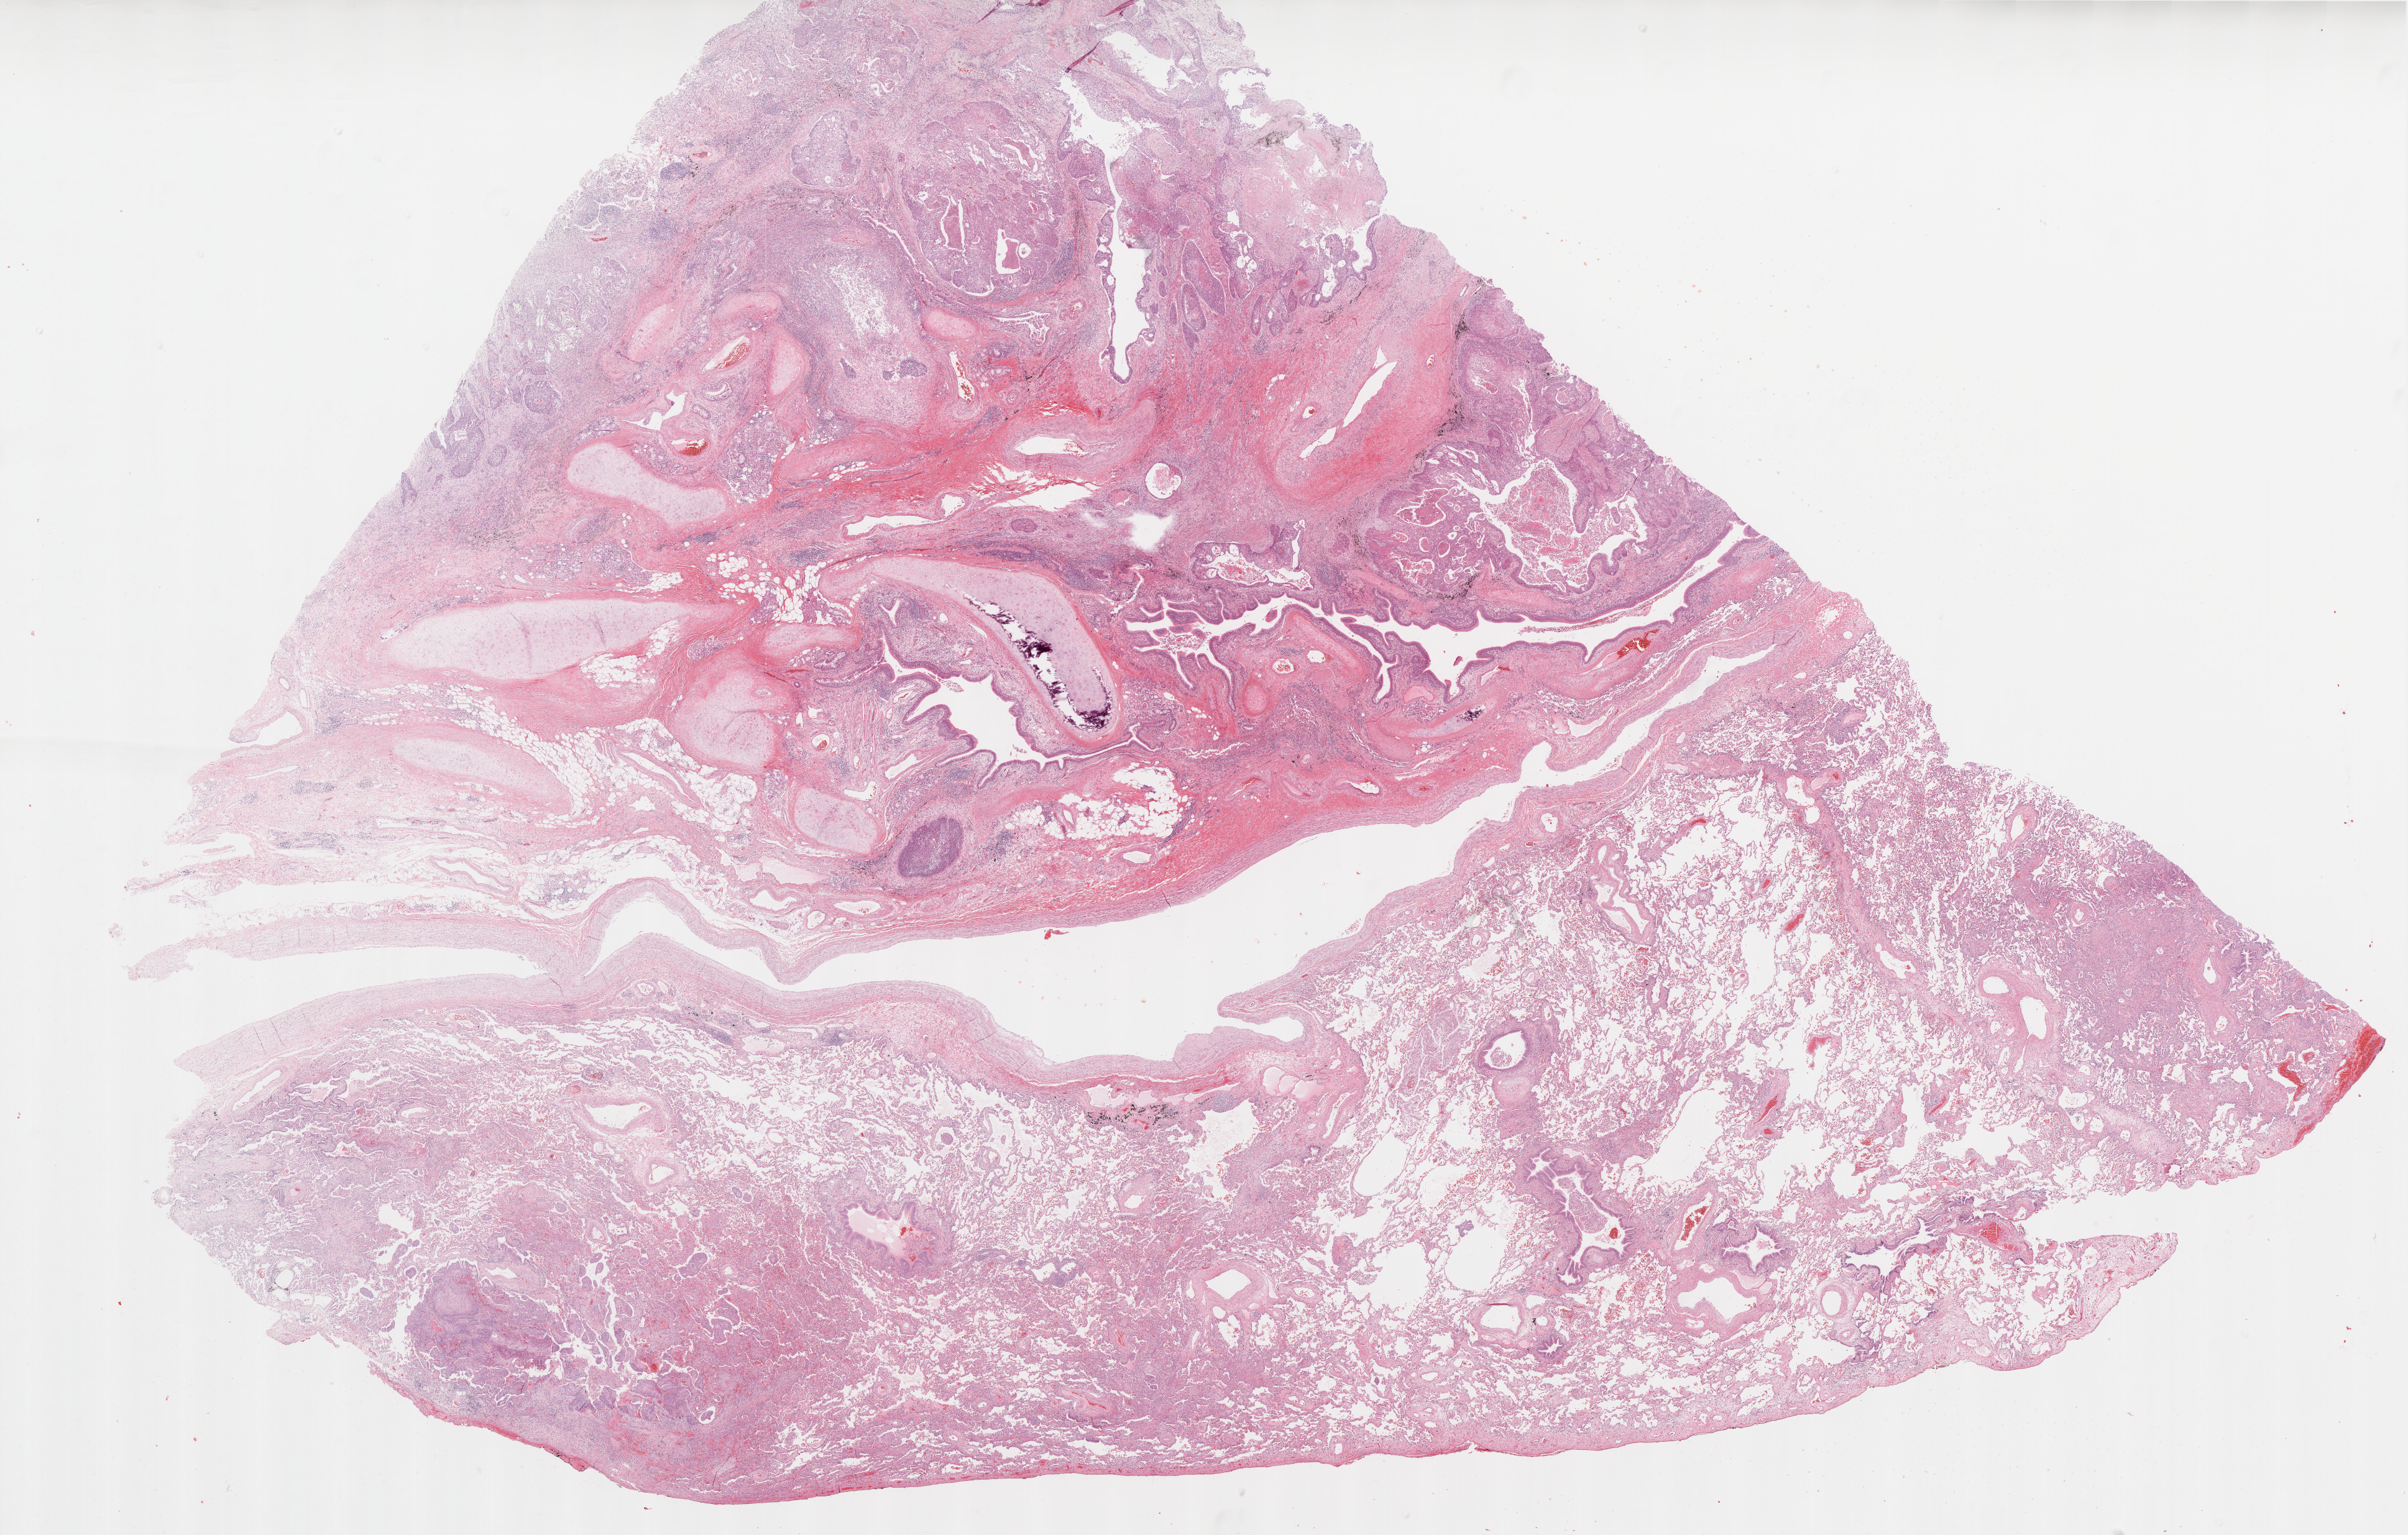
H&E whole-slide image — low-resolution overview of the scanned area, about 31.1 x 19.9 mm (slide scanned at 20x). Formalin-fixed paraffin-embedded (FFPE) diagnostic section. Lung, primary tumour sample. Male patient; age at initial diagnosis 70 years.
Pathologic diagnosis: Squamous cell carcinoma, NOS (upper lobe, lung).